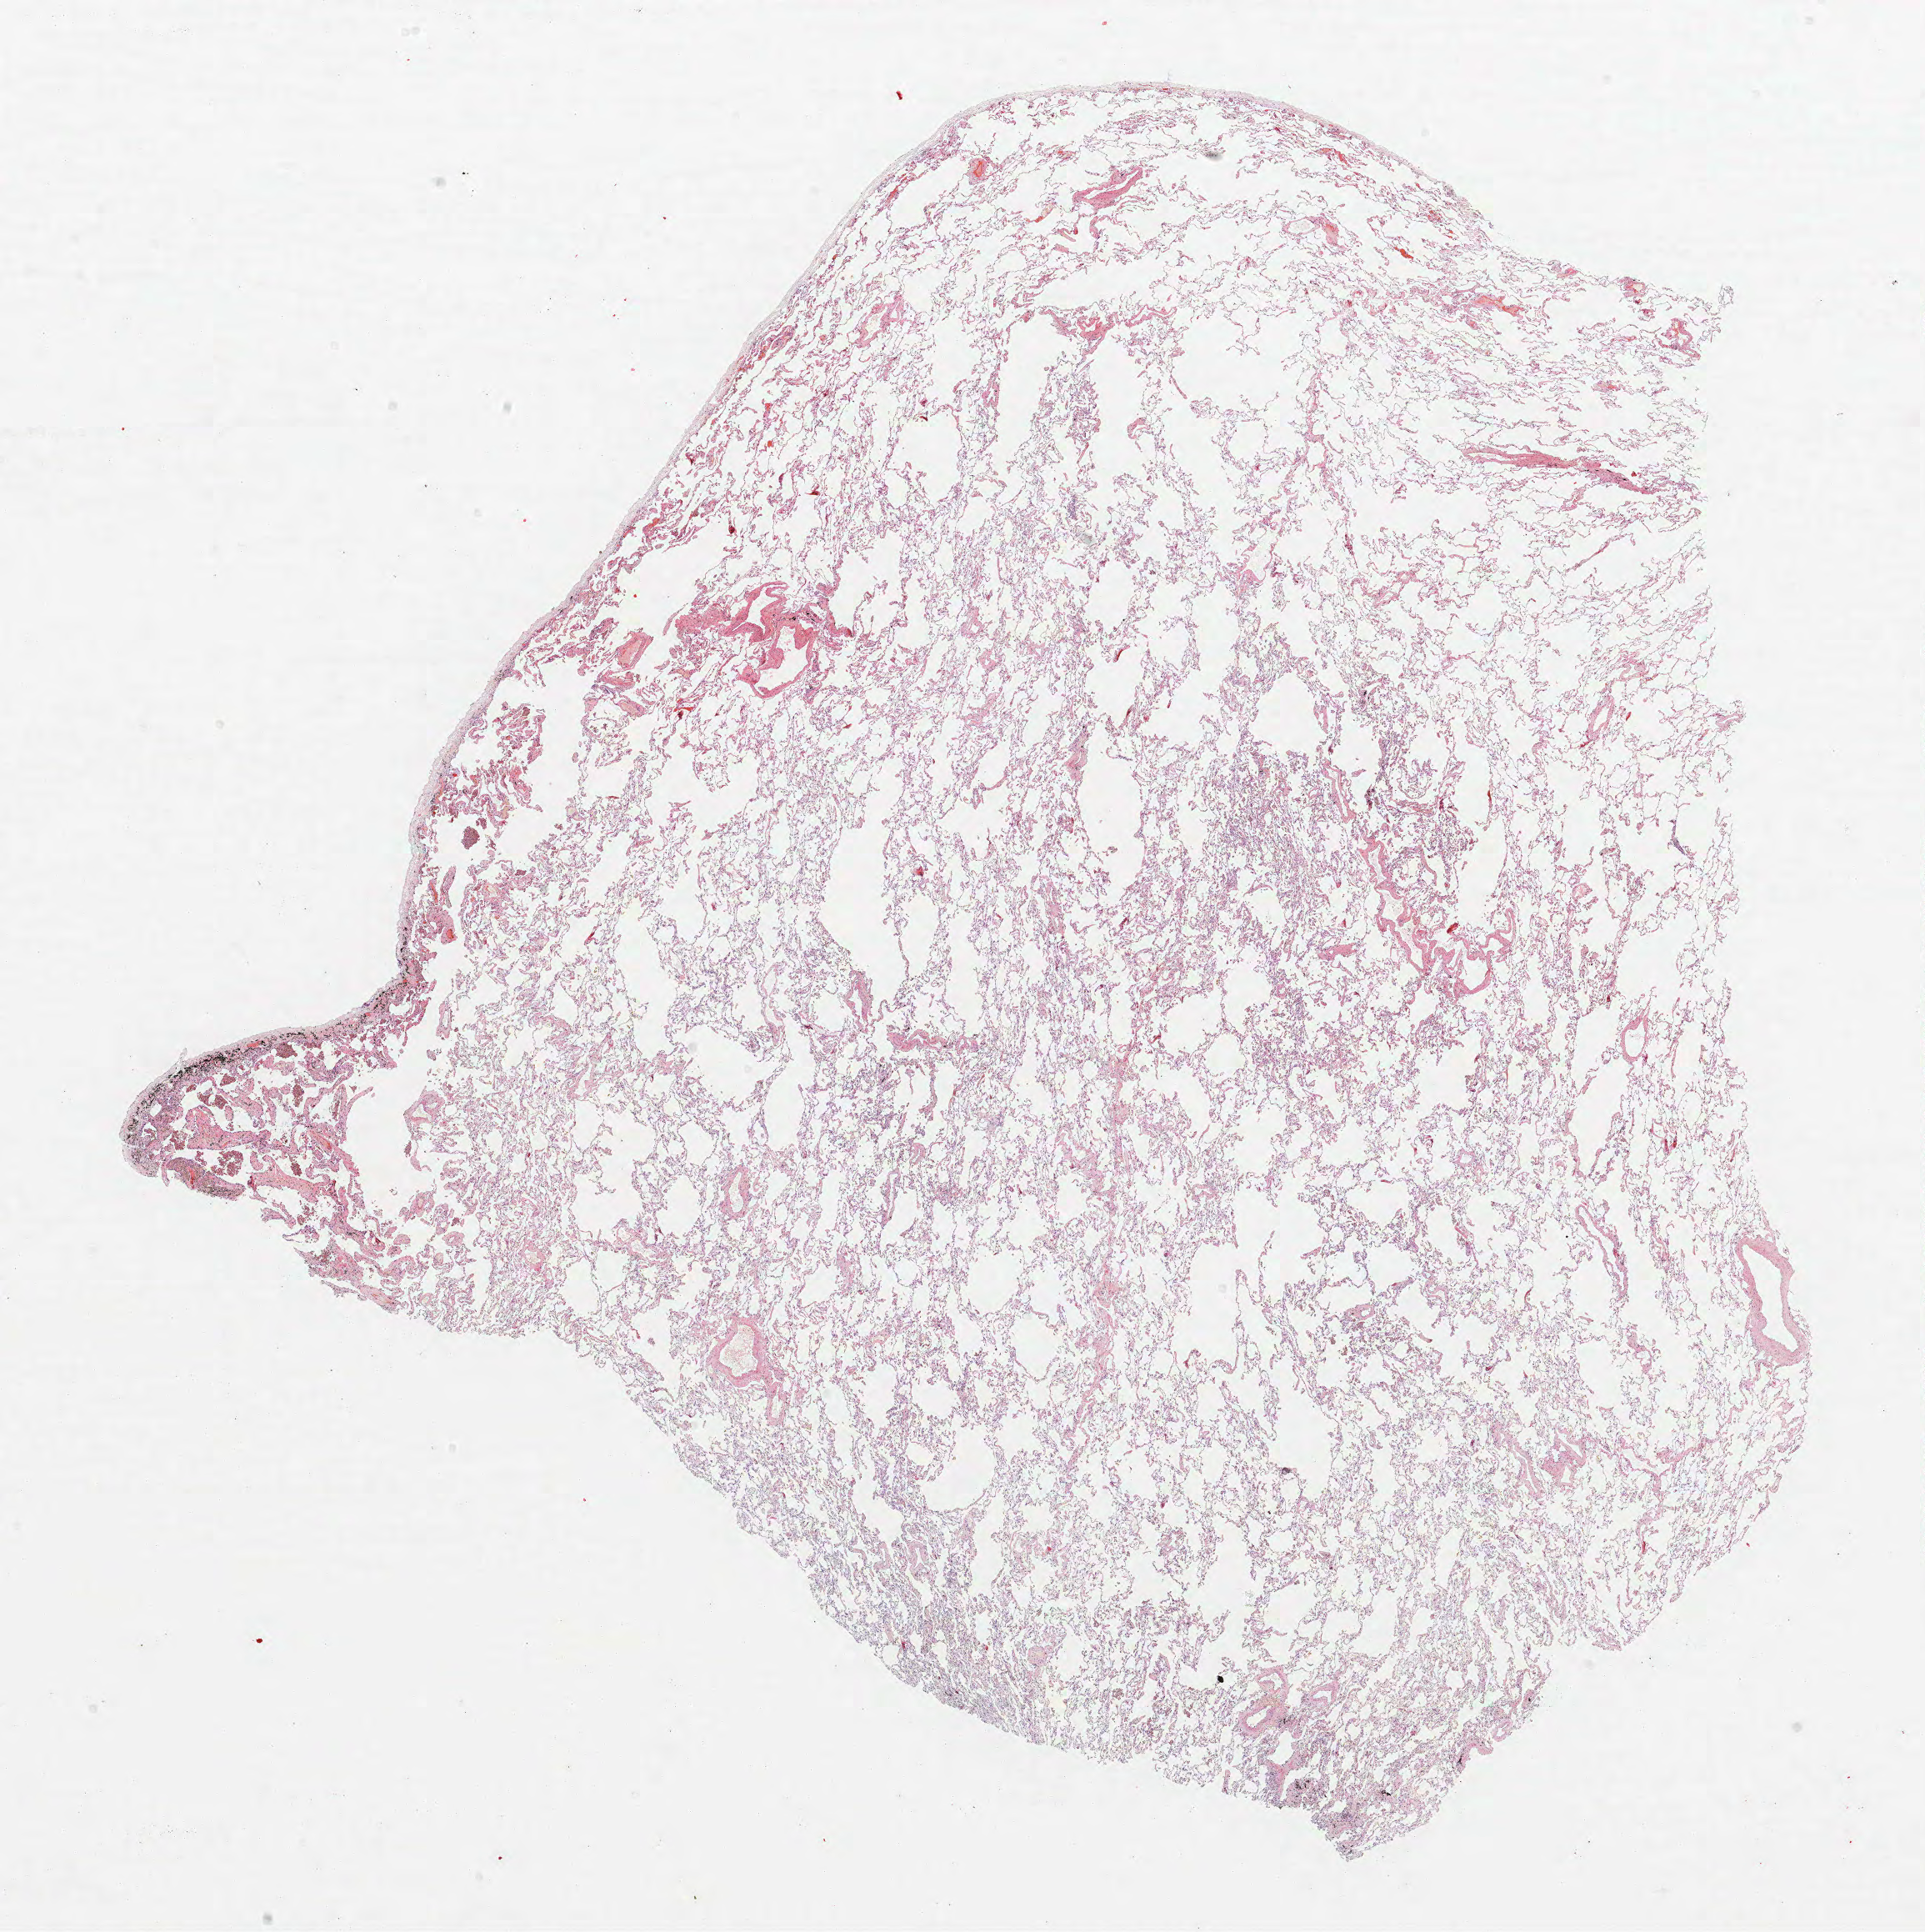
Whole-slide histology image, Hematoxylin and eosin (H&E) stained, whole scanned area (about 18.5 x 18.5 mm, slide scanned at 40x) shown as a low-resolution overview. Formalin-fixed paraffin-embedded (FFPE) section. Lung tissue. Male patient, aged 58 at enrolment. Current smoker at enrolment. Grade: moderately differentiated (G2).
Stage (AJCC 6th edition): IA. Participant's lung-cancer diagnosis: Bronchiolo-alveolar adenocarcinoma, NOS. Primary tumour location (clinical record): right upper lobe. ICD-O-3 topography: upper lobe of lung (C34.1). Tumour size (pathology): 6 mm. Note: participant had 2 primary lung cancers recorded; fields above describe the first.